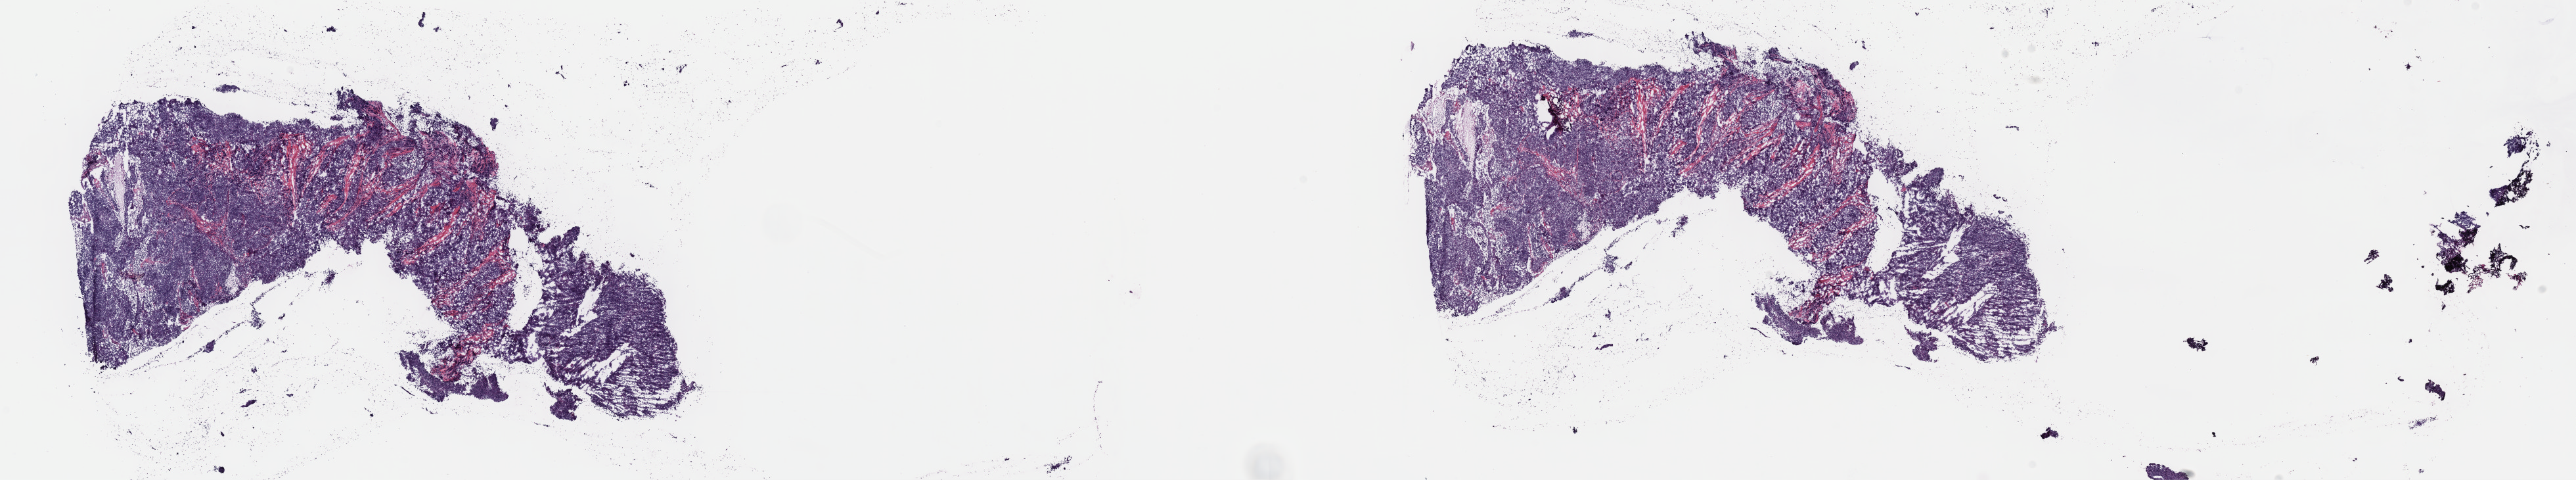
Whole-slide histology image, Hematoxylin and eosin (H&E) stained — low-resolution overview of the scanned area, about 31.7 x 5.9 mm. Frozen section. Primary tumour sample from the thymus. Patient: female, age at initial diagnosis 65 years. Composition of this section per pathologist review: tumour cells 90%, tumour nuclei 95%, normal cells 0%, stromal cells 10%, necrosis 0%. Inflammatory infiltration, as recorded: lymphocyte infiltration 0%, monocyte infiltration 0%, neutrophil infiltration 0%.
* histologic diagnosis: Thymoma, type B3, malignant